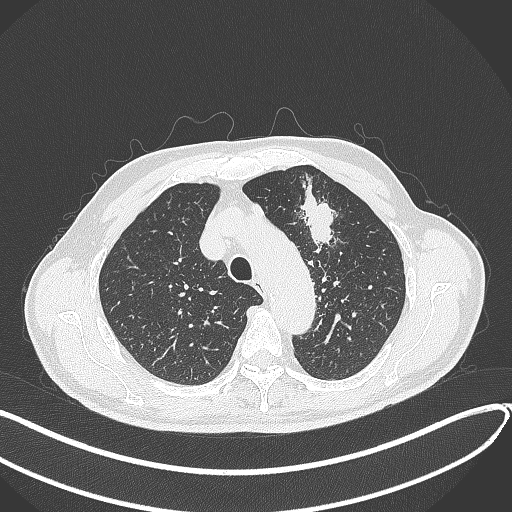
Chest CT, one axial slice; slice 321 of 459 in the series (ordered by position); reconstruction kernel B70f; 120 kVp; lung window (W 1500 / L -600 HU); 512 × 512 image matrix. Male patient, age 74 years. Case-level facts recorded for this patient, not image findings: clinical TNM (as recorded): T2b N0 M1c.
Structures marked on this image (bounding box drawn by a radiologist):
- lung tumour (recorded histology: adenocarcinoma): box from (x=296, y=178) to (x=337, y=255) px